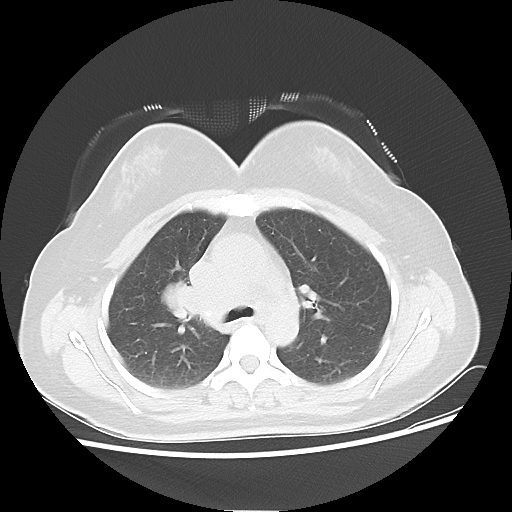
Chest CT, one axial slice; position 34 of 50 along the scan axis; reconstruction kernel LUNG; 100 kVp; lung window (W 1500 / L -600 HU); 5 mm slice thickness; 512 × 512 image matrix, field of view 360 × 360 mm. Patient: female, 40 years. Case-level facts recorded for this patient, not image findings: clinical TNM (as recorded): T1c N3 M0; histopathological grade: G3.
Outlined on this slice (bounding box drawn by a radiologist):
- lung tumour (recorded histology: small cell carcinoma): bounding box <157,282,197,327> (left, top, right, bottom; pixels)